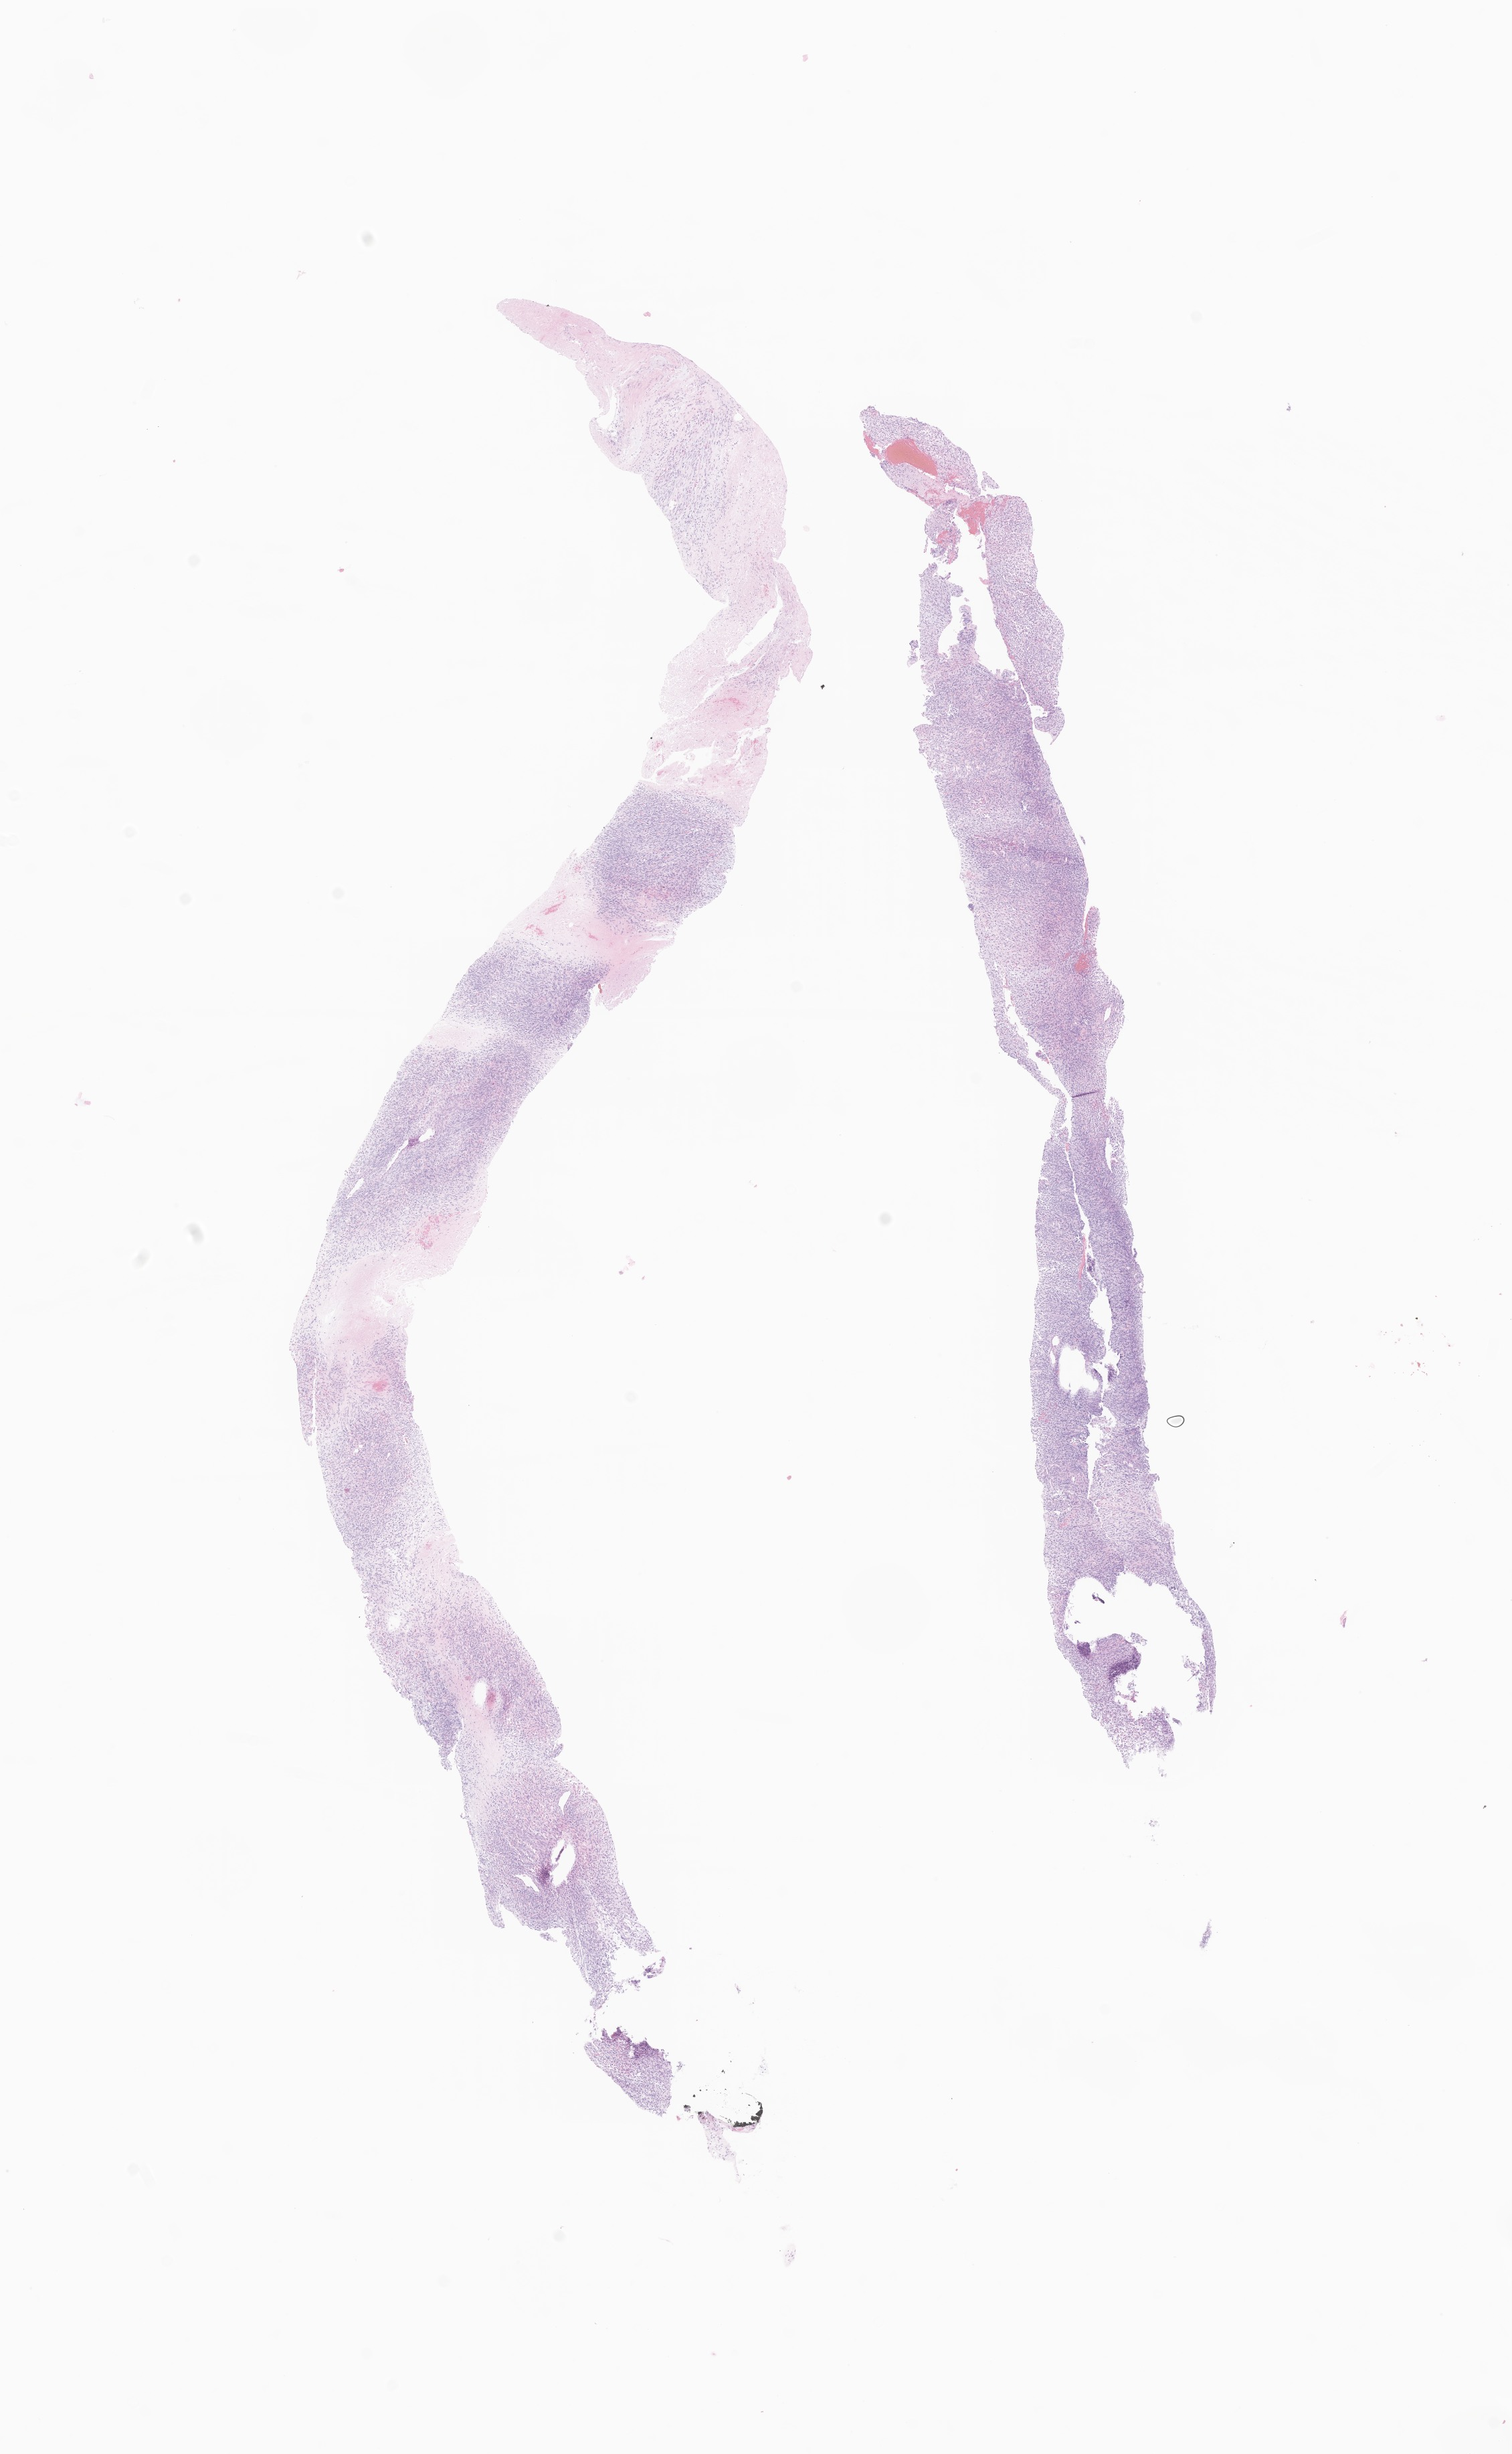
Whole-slide image, hematoxylin and eosin (H&E) stain of tumor tissue from the nasopharynx, shown as a low-resolution overview of the whole scanned area (about 9.5 x 15.5 mm); formalin-fixed, paraffin-embedded (FFPE) tissue. Patient: female, age 79 months (6 years 7 months).
Recorded diagnosis: Rhabdomyosarcoma, NOS.